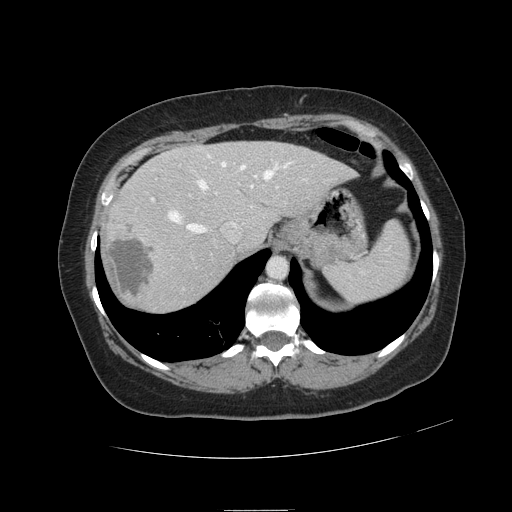
Contrast-enhanced abdominal CT, one axial slice. Slice 91 of 121 in the series (ordered by position). 120 kVp. Soft-tissue window (W 400 / L 40 HU). 2.5 mm slice thickness. 512 × 512 image matrix. Female patient, age 52 years. From the clinical record (not read from this slice): diagnosis: colorectal cancer liver metastases, imaged before liver resection; multiple liver metastases: yes; largest metastasis: 6.3 cm; disease in both lobes: no.
Structures marked on this image (expert manual segmentation):
- hepatic veins: box from (x=169, y=154) to (x=290, y=233) px
- liver: (x=105, y=142)–(x=352, y=312)
- planned liver remnant (the part of the liver to remain after resection): (x=168, y=142)–(x=353, y=247)
- portal vein (with intrahepatic branches): (x=151, y=186)–(x=278, y=290)
- liver metastasis: (x=108, y=231)–(x=154, y=297)